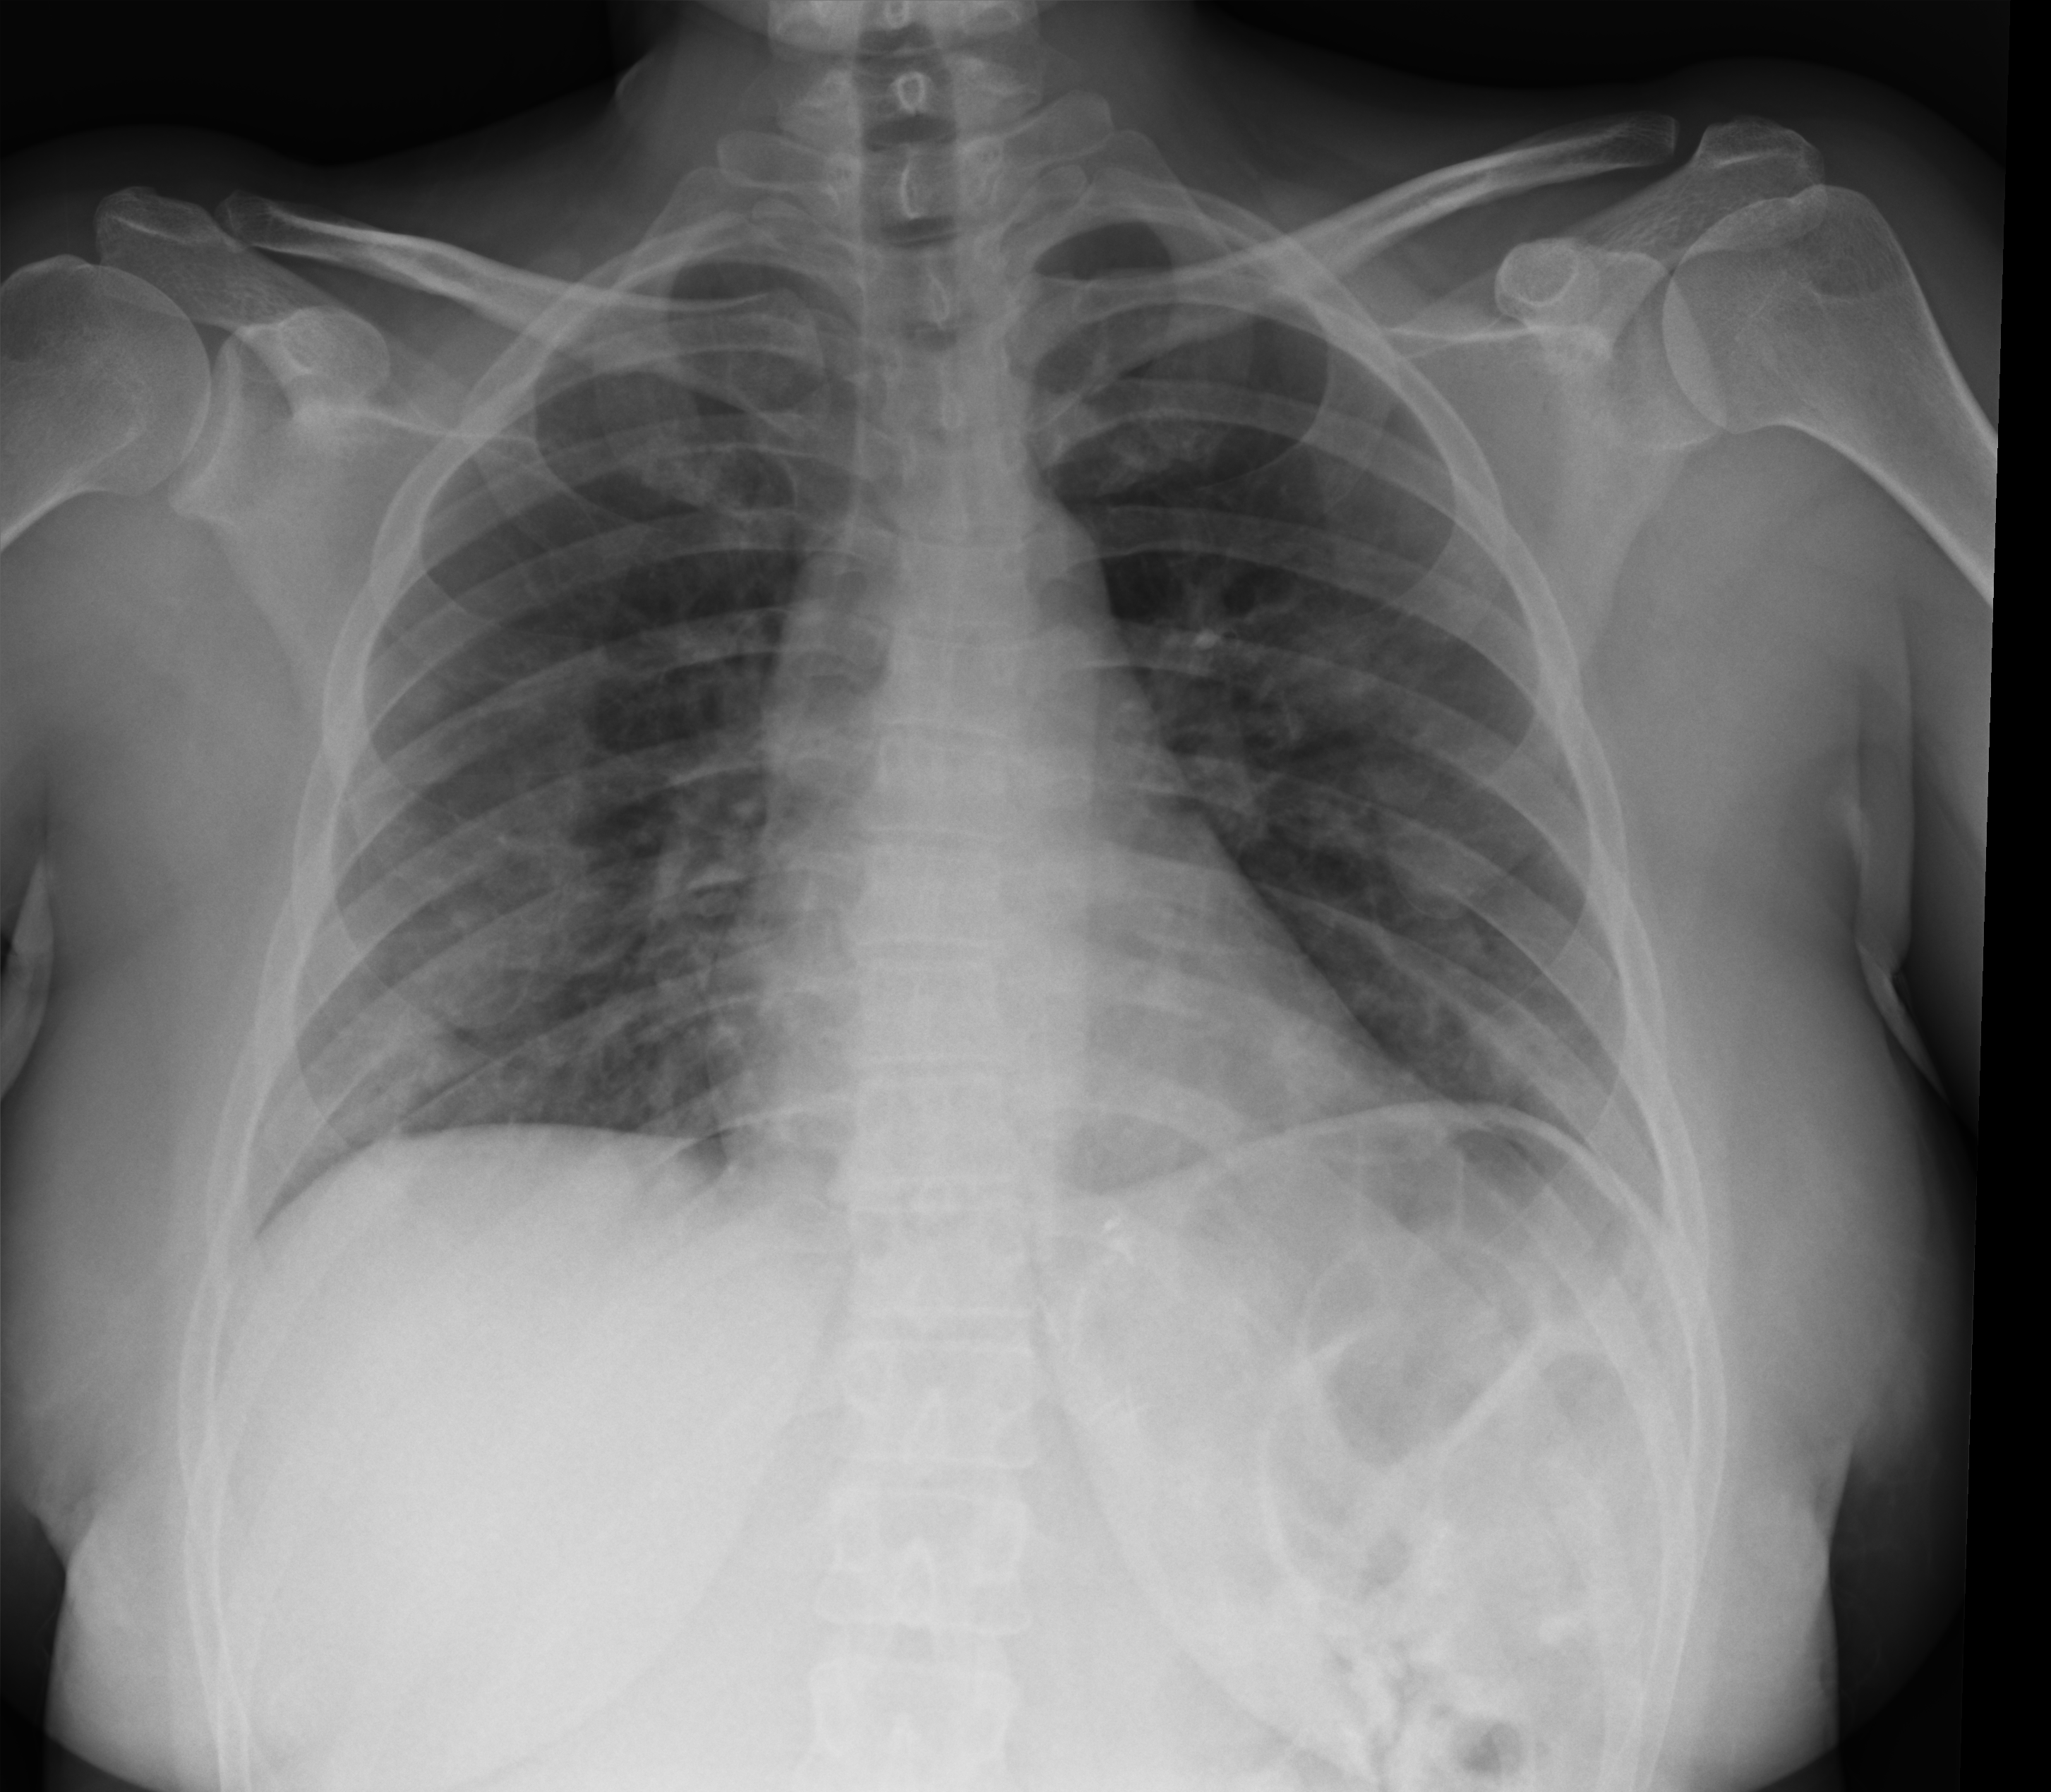
Portable chest radiograph; anteroposterior (AP) projection. Female patient hospitalised with COVID-19, age 18–59 years.
From the hospital-stay record, not from the radiograph (when in the stay this image was taken is not recorded):
- other chronic lung disease (admission record): no